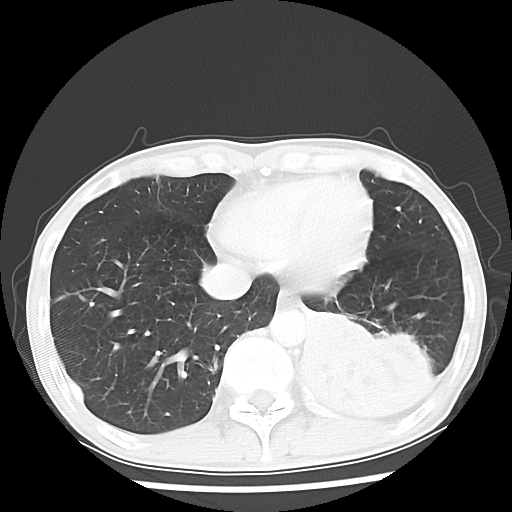
Chest CT, one axial slice. Slice 15 of 64 in the series (ordered by position). 120 kVp. Lung window (W 1500 / L -600 HU). 512 × 512 image matrix, field of view 313 × 313 mm. Patient: male, 68 years. From the clinical record (not read from this slice): clinical TNM (as recorded): T4 N0 M0.
Outlined on this slice (bounding box drawn by a radiologist):
- lung tumour (recorded histology: squamous cell carcinoma): bounding box <286,301,454,428> (left, top, right, bottom; pixels)